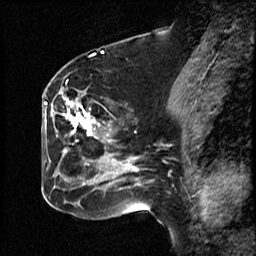
Breast MRI (dynamic contrast-enhanced), one sagittal slice. Position 27 of 50 along the scan axis. Dynamic contrast-enhanced study with each time point stored as its own series, time point 2 of 4 at this slice position (early post-contrast, ordered by acquisition time). 1.5 T. TE 4.2 ms, TR 18.5 ms. 256 × 256 image matrix, field of view 200 × 200 mm. Female patient, age 44 years. From the clinical record (not read from this slice): setting: breast cancer imaged before/during neoadjuvant chemotherapy; receptor status: HR-positive, HER2-negative.
Outlined on this slice (semi-automatically segmented with operator editing):
- analysis volume of interest (the breast-tissue region the enhancement analysis was run in; not a lesion): bounding box [x1, y1, x2, y2] px = [59, 81, 114, 206]
- tumour enhancement mask (voxels above the 100 % enhancement threshold inside the analysis volume of interest): [63, 96, 114, 177]